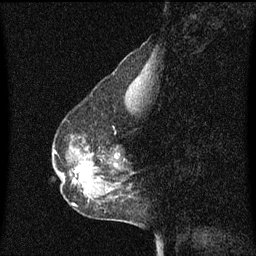
Breast MRI (dynamic contrast-enhanced), one sagittal slice. Position 21 of 60 along the scan axis. Dynamic contrast-enhanced series, image 2 of 3 at this slice position (ordered by acquisition). 1.5 T. TE 4.2 ms, TR 8.4 ms. 256 × 256 image matrix. Female patient, age 50 years. From the clinical record (not read from this slice): setting: breast cancer imaged before/during neoadjuvant chemotherapy; receptor status: HR-positive, HER2-negative.
Annotated regions visible in this slice (semi-automatically segmented with operator editing):
- analysis volume of interest (the breast-tissue region the enhancement analysis was run in; not a lesion): bounding box [x1, y1, x2, y2] px = [61, 144, 124, 189]
- tumour enhancement mask (voxels above the 70 % enhancement threshold inside the analysis volume of interest): [74, 164, 117, 183]